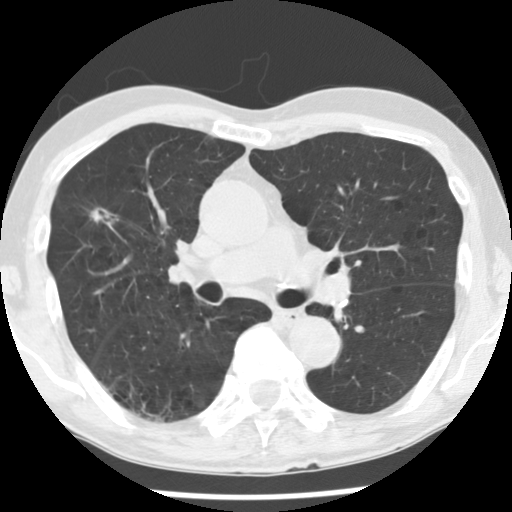
Low-dose screening chest CT, one axial slice. Position 101 of 176 along the scan axis. Lung window (W 1500 / L -600 HU). 2.5 mm slice thickness. 512 × 512 image matrix, field of view 309 × 309 mm.
Structures marked on this image (expert manual segmentation):
- lesion 1 (tumor, upper lobe of right lung): bounding box <90,208,108,223> (left, top, right, bottom; pixels)